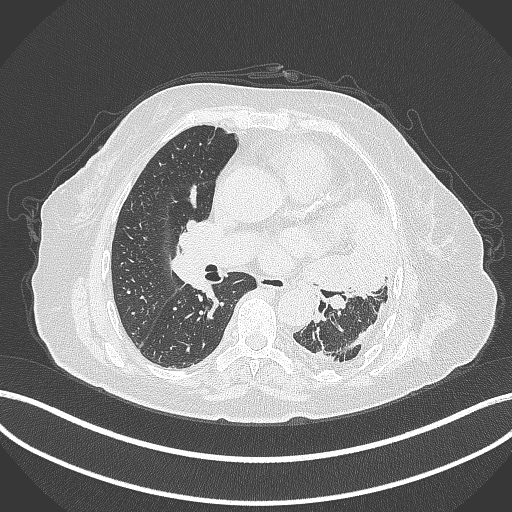
Chest CT, one axial slice. Position 193 of 399 along the scan axis. 120 kVp. Lung window (W 1500 / L -600 HU). 1 mm slice thickness. 512 × 512 image matrix, field of view 400 × 400 mm. Patient: female, 75 years. Case-level facts recorded for this patient, not image findings: clinical TNM (as recorded): T3 N3 M1.
Outlined on this slice (rectangle marked by the reading radiologist):
- lung tumour (recorded histology: adenocarcinoma): bounding box (x1, y1, x2, y2) in pixels: (305, 195, 399, 296)